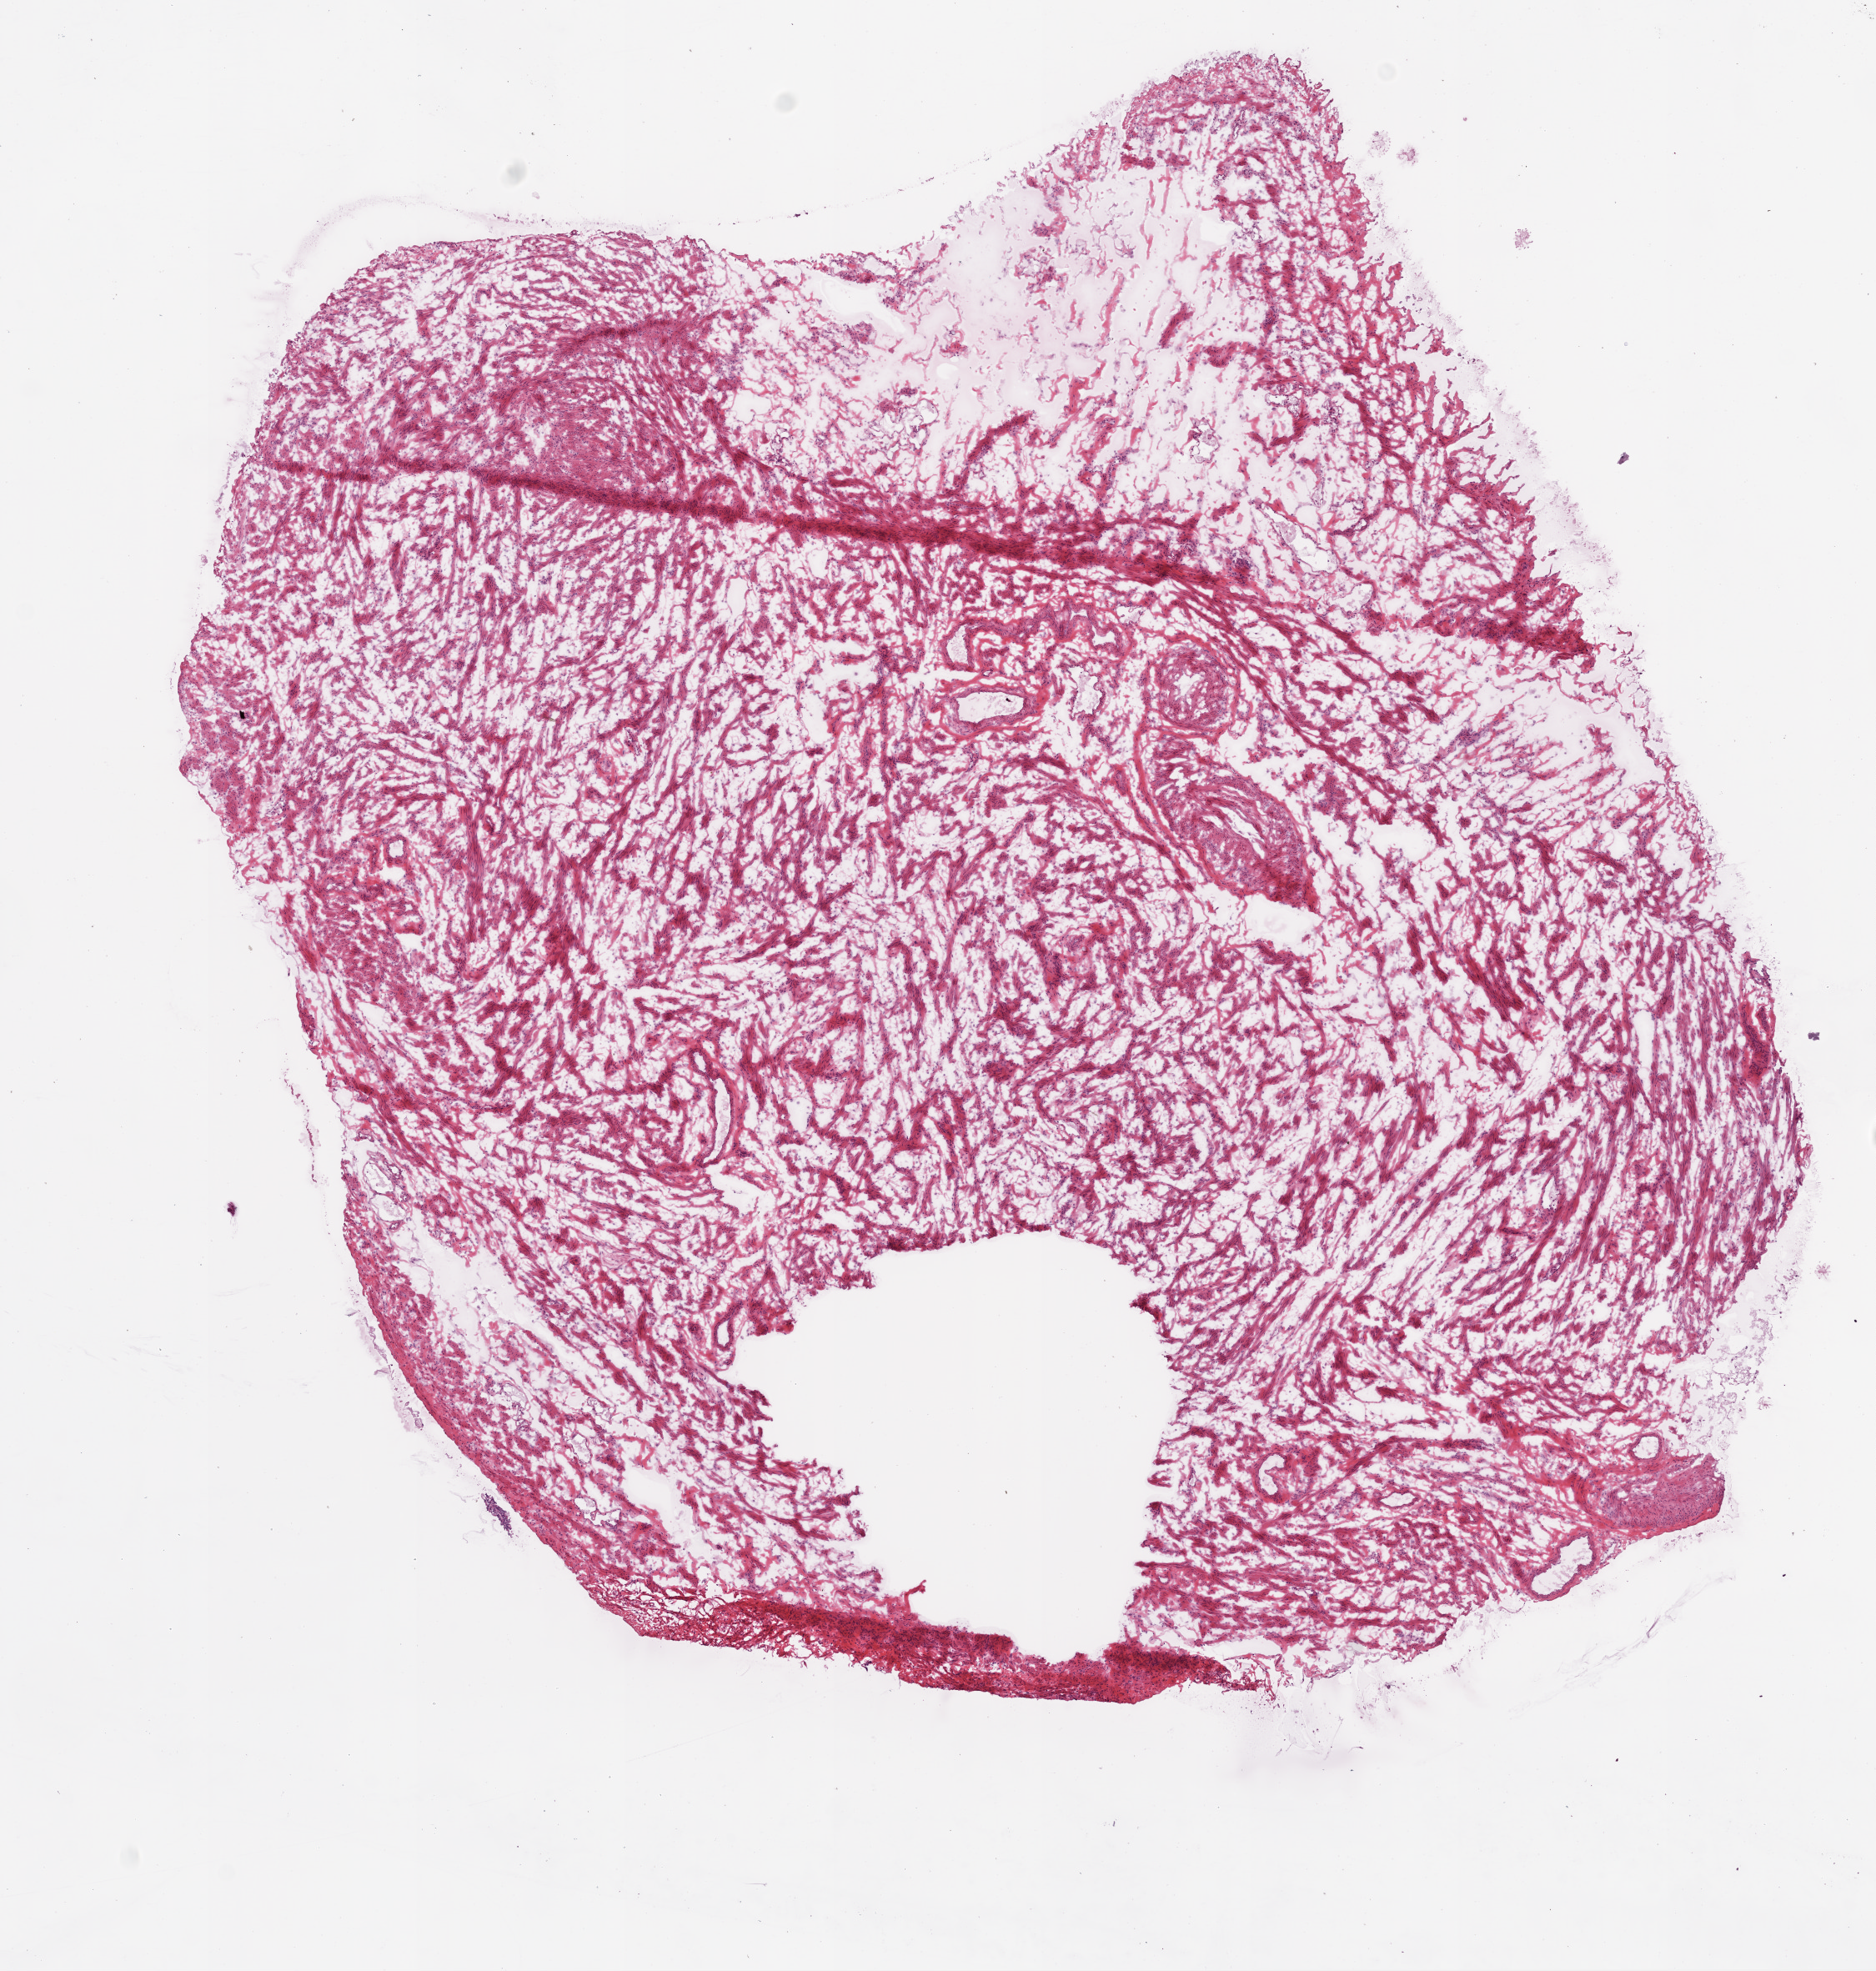
Digitized Hematoxylin and eosin (H&E) stained tissue section (whole slide), whole scanned area (about 9.0 x 9.5 mm) shown as a low-resolution overview; frozen section from the bottom of the tissue portion; sample: solid tissue normal (non-tumour tissue), ovary. Female, age 62 years at initial diagnosis.
- this section: solid tissue normal (non-tumour) sample from the same patient
- patient diagnosis: Serous cystadenocarcinoma, NOS